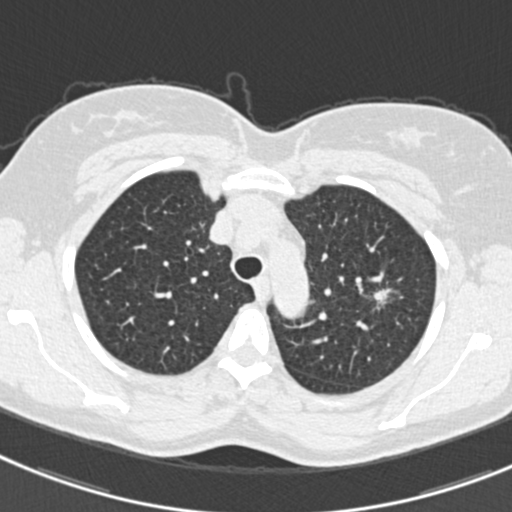
Low-dose screening chest CT, one axial slice; slice 246 of 309 in the series (ordered by position); reconstruction kernel B30f; lung window (W 1500 / L -600 HU); 512 × 512 image matrix, field of view 302 × 302 mm.
Annotated regions visible in this slice (expert manual segmentation):
- lesion 1 (tumor, upper lobe of left lung): box from (x=373, y=288) to (x=390, y=304) px